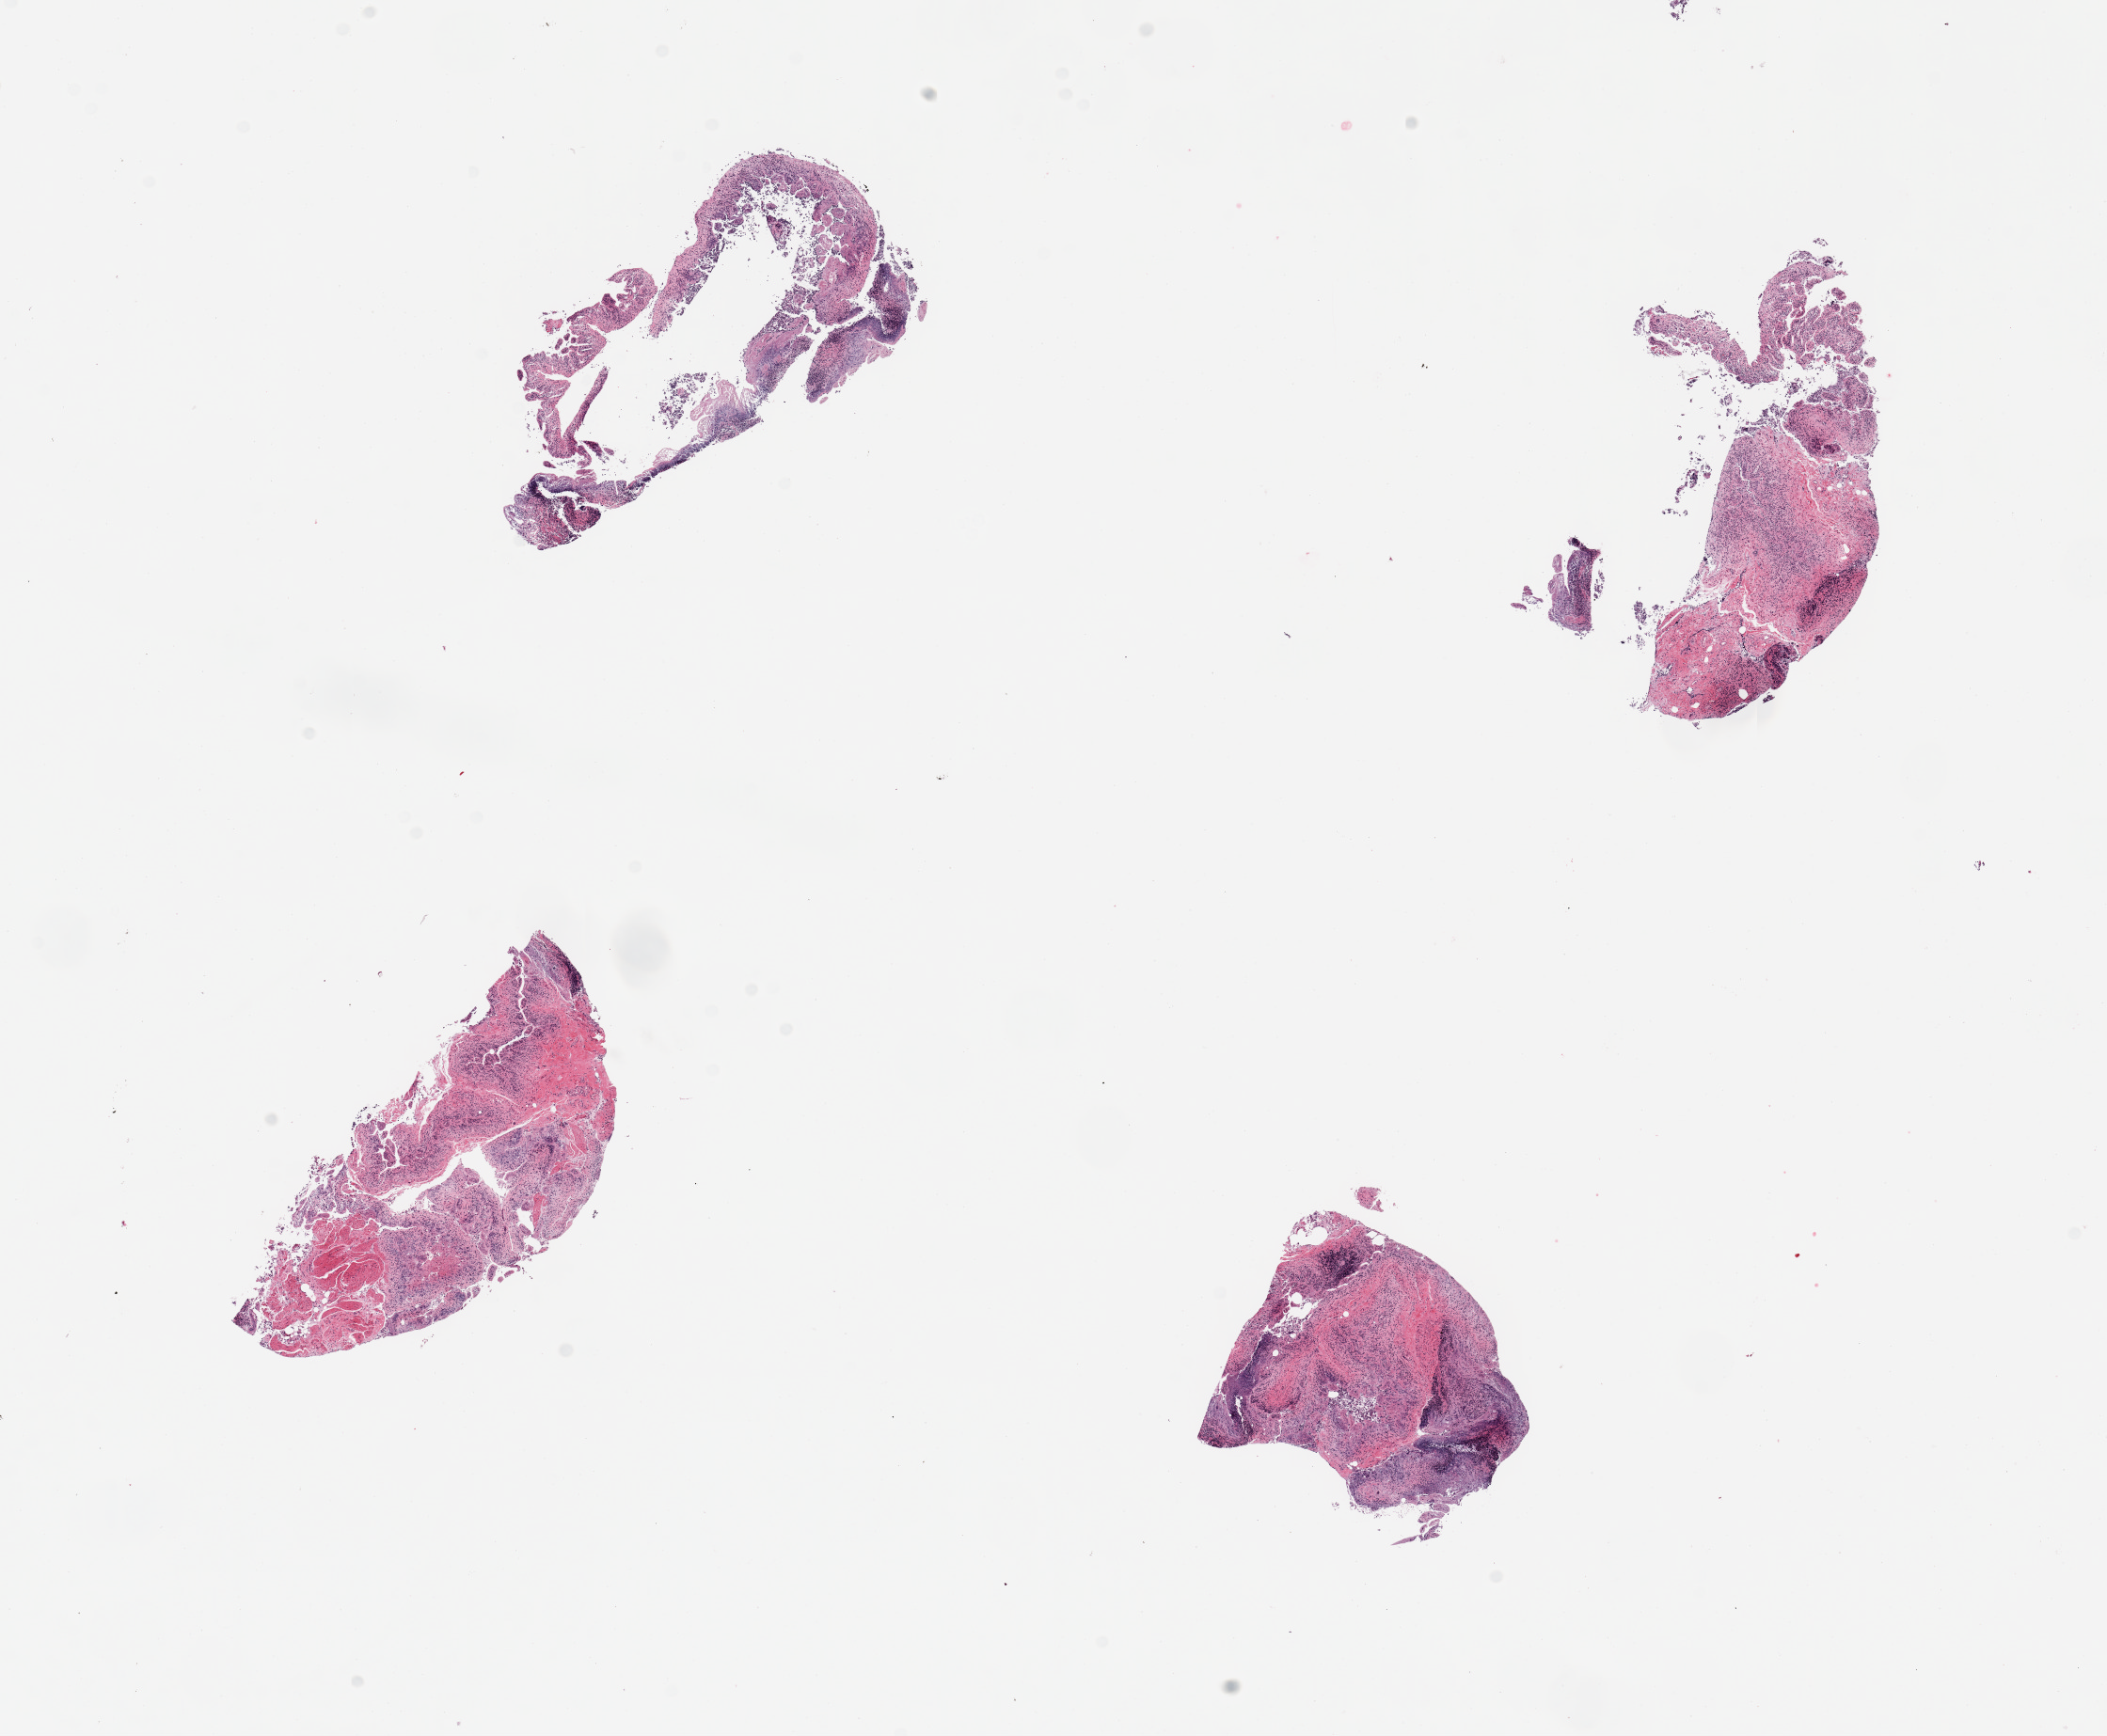
Whole-slide image, hematoxylin and eosin (H&E) stain, whole scanned area (about 17.7 x 14.6 mm) shown as a low-resolution overview. Female donor.
Specimen: PAXgene-fixed paraffin-embedded (PFPE) section; target tissue: ileum; tissue donor sample.